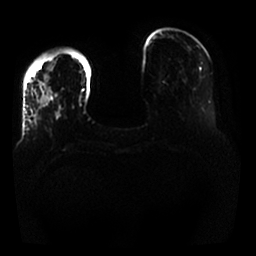
Breast MRI, one axial slice. Position 3 of 25 along the scan axis. Diffusion-weighted series; image 2 of 4 stored at this slice position (different b-values; order by instance number). 1.5 T. 4 mm slice thickness. 256 × 256 image matrix, field of view 350 × 350 mm. Female patient.
Outlined on this slice (outlined manually by an expert reader):
- tumour on diffusion-weighted imaging: bounding box (x1, y1, x2, y2) in pixels: (39, 74, 50, 107)